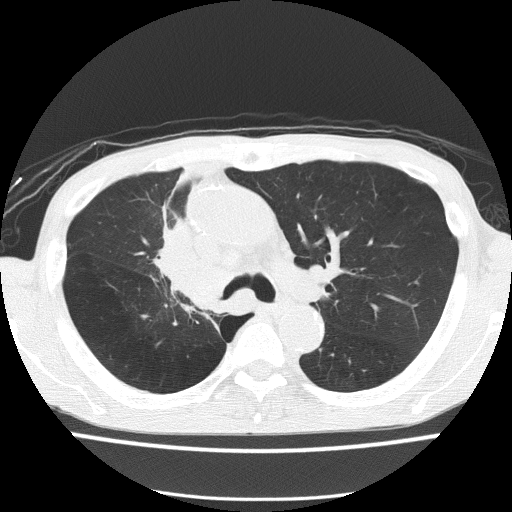
Axial slice from a low-dose chest CT screening exam; baseline screening round; lung window (W 1500 / L -600 HU); 2 mm slice thickness; lung (sharp) reconstruction kernel (FC51); slice 52 of 150 in the series; 512 × 512 image matrix. Male participant, aged 59 years at enrolment. Former smoker at enrolment.
- Expert reader's lesion annotation, bounding box [x1, y1, x2, y2] px = [139, 231, 233, 322].
- The screening reader recorded 5 non-calcified nodules or masses ≥4 mm on this exam (left upper lobe, left upper lobe, left upper lobe, right middle lobe, right lower lobe); which of them this box marks is not recorded.
- Official screen result: positive, change unspecified: nodule(s) >= 4 mm or enlarging nodule(s), mass(es), or other non-specific abnormalities suspicious for lung cancer.
- Later outcome: lung cancer diagnosed 72 days after this screen — squamous cell carcinoma, NOS, right upper lobe, moderately differentiated (G2), stage IV (AJCC 6th edition).